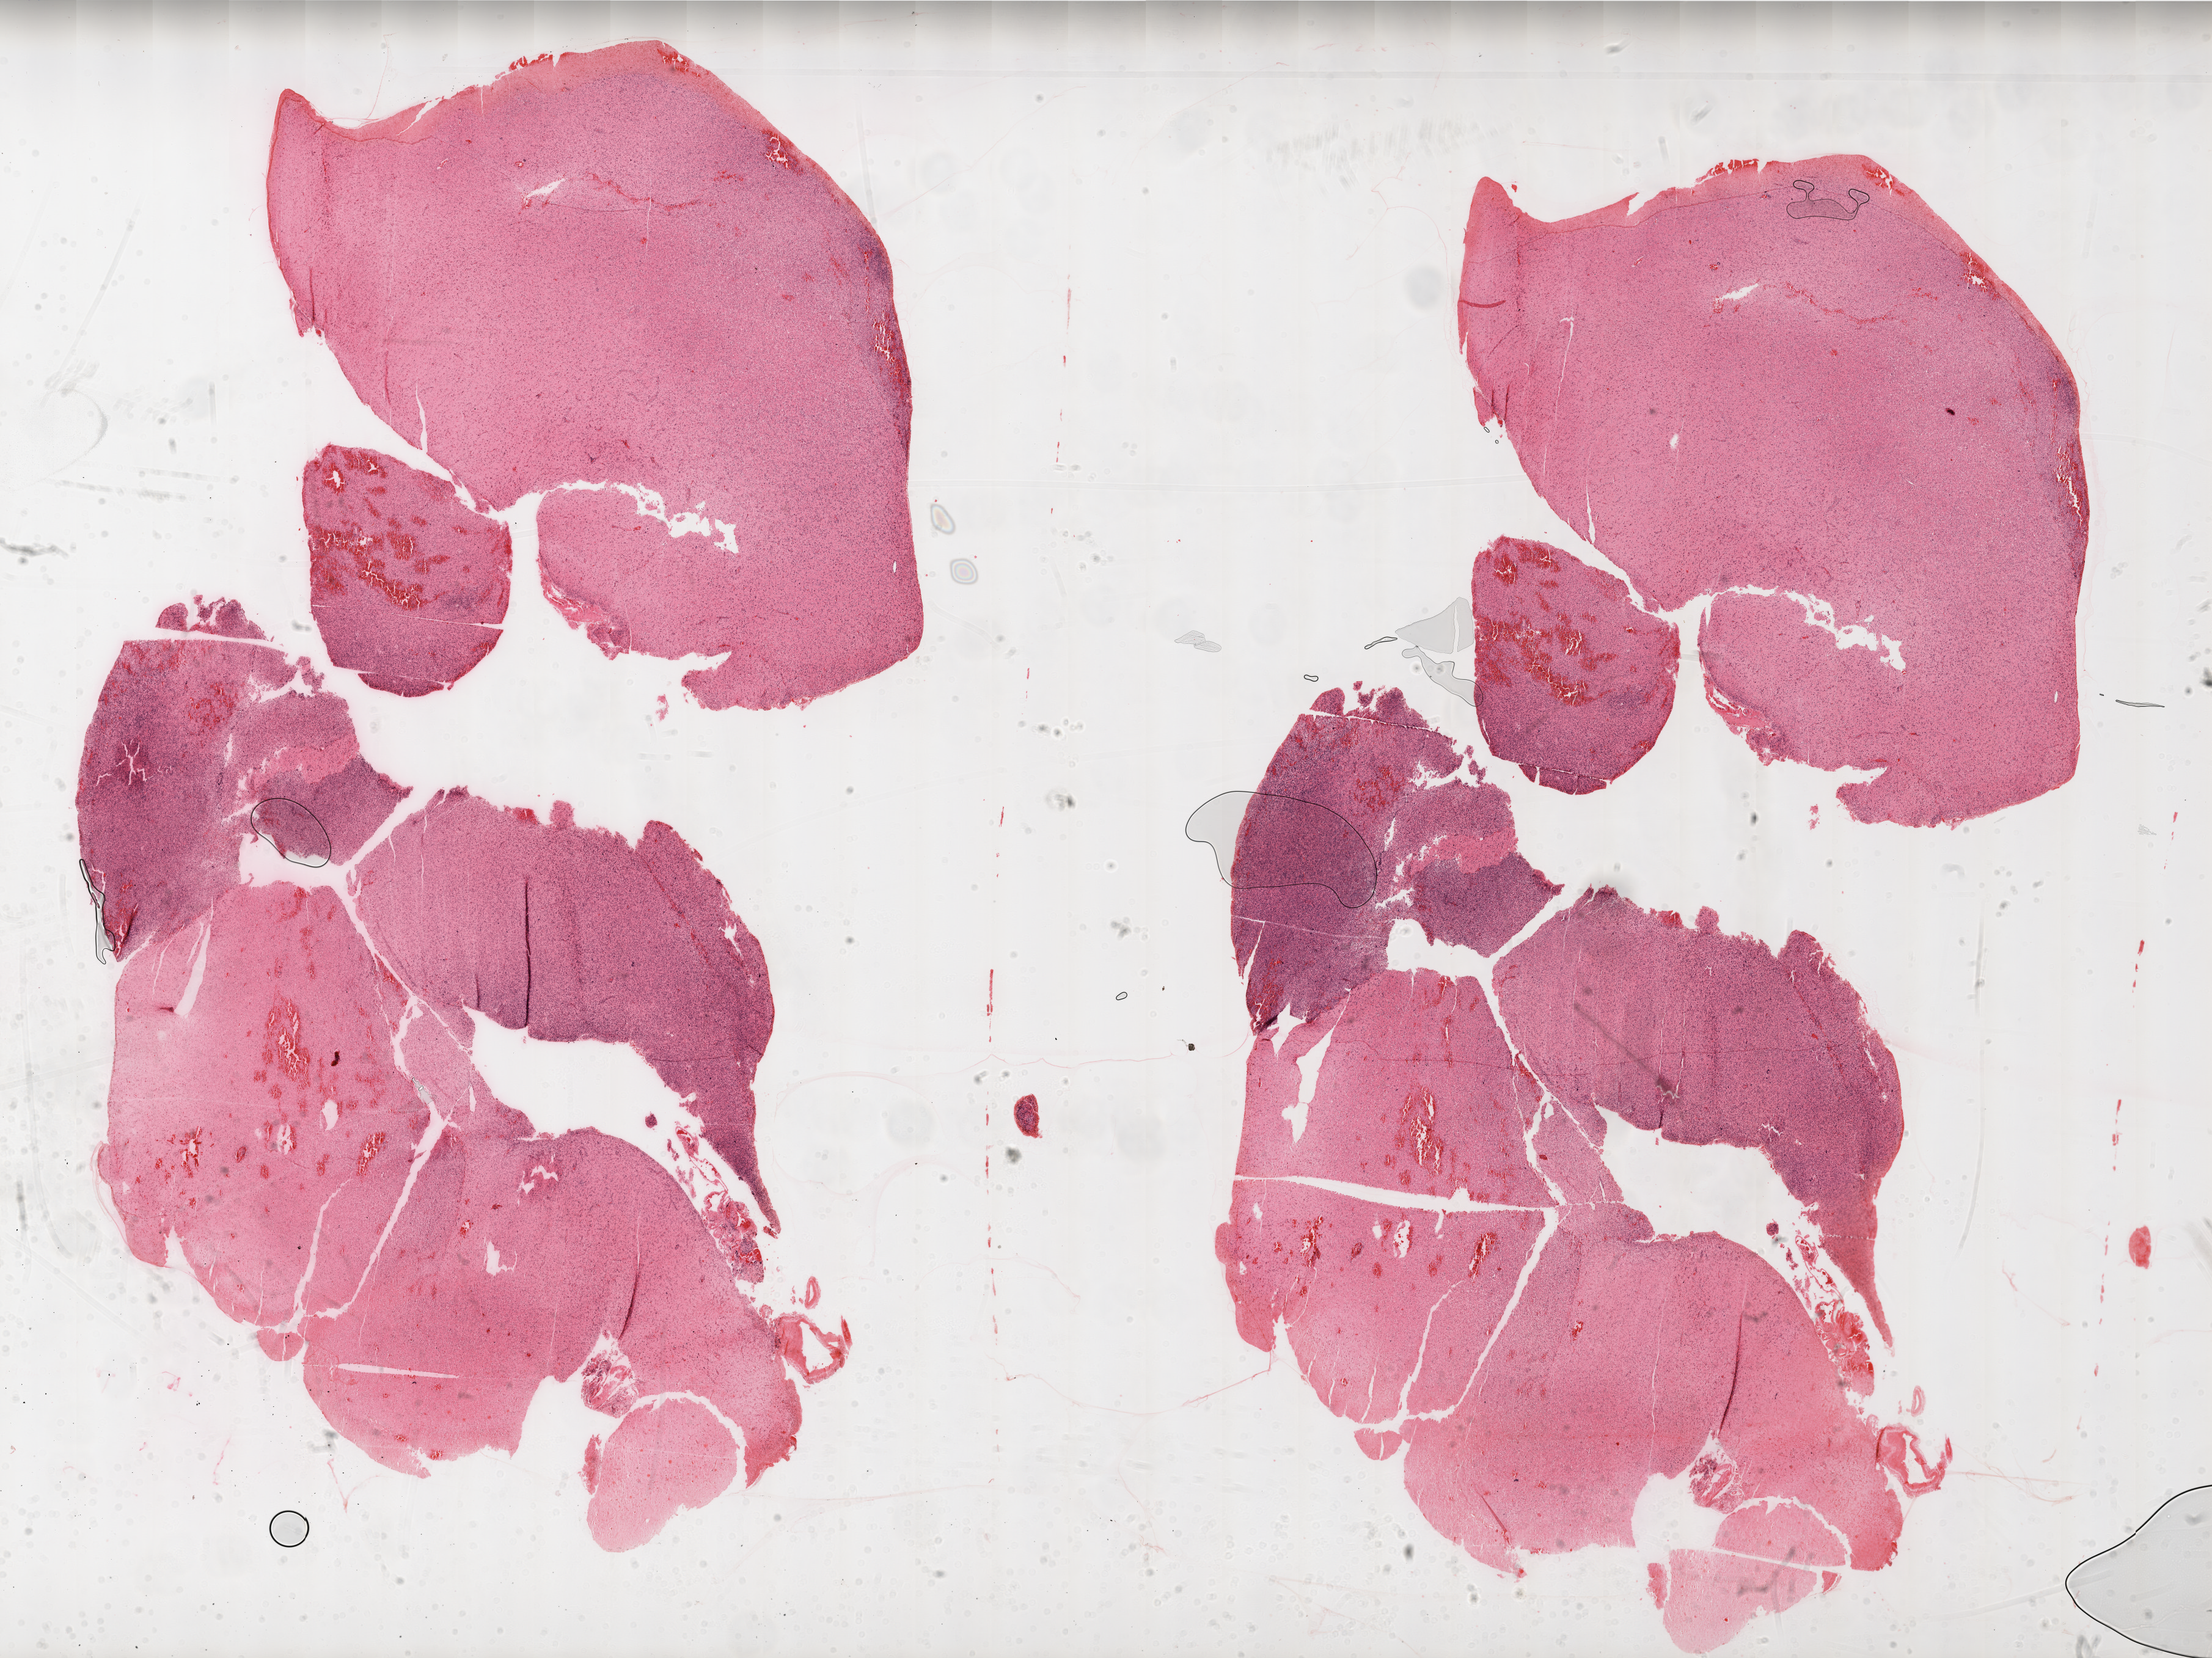
Digitized Hematoxylin and eosin (H&E) stained tissue section (whole slide), shown as a low-resolution overview of the whole scanned area (about 29.0 x 21.7 mm, acquisition: 20x scan), FFPE section, sample: primary tumour, brain. Male, age 63 years at initial diagnosis.
Diagnosis: Glioblastoma.